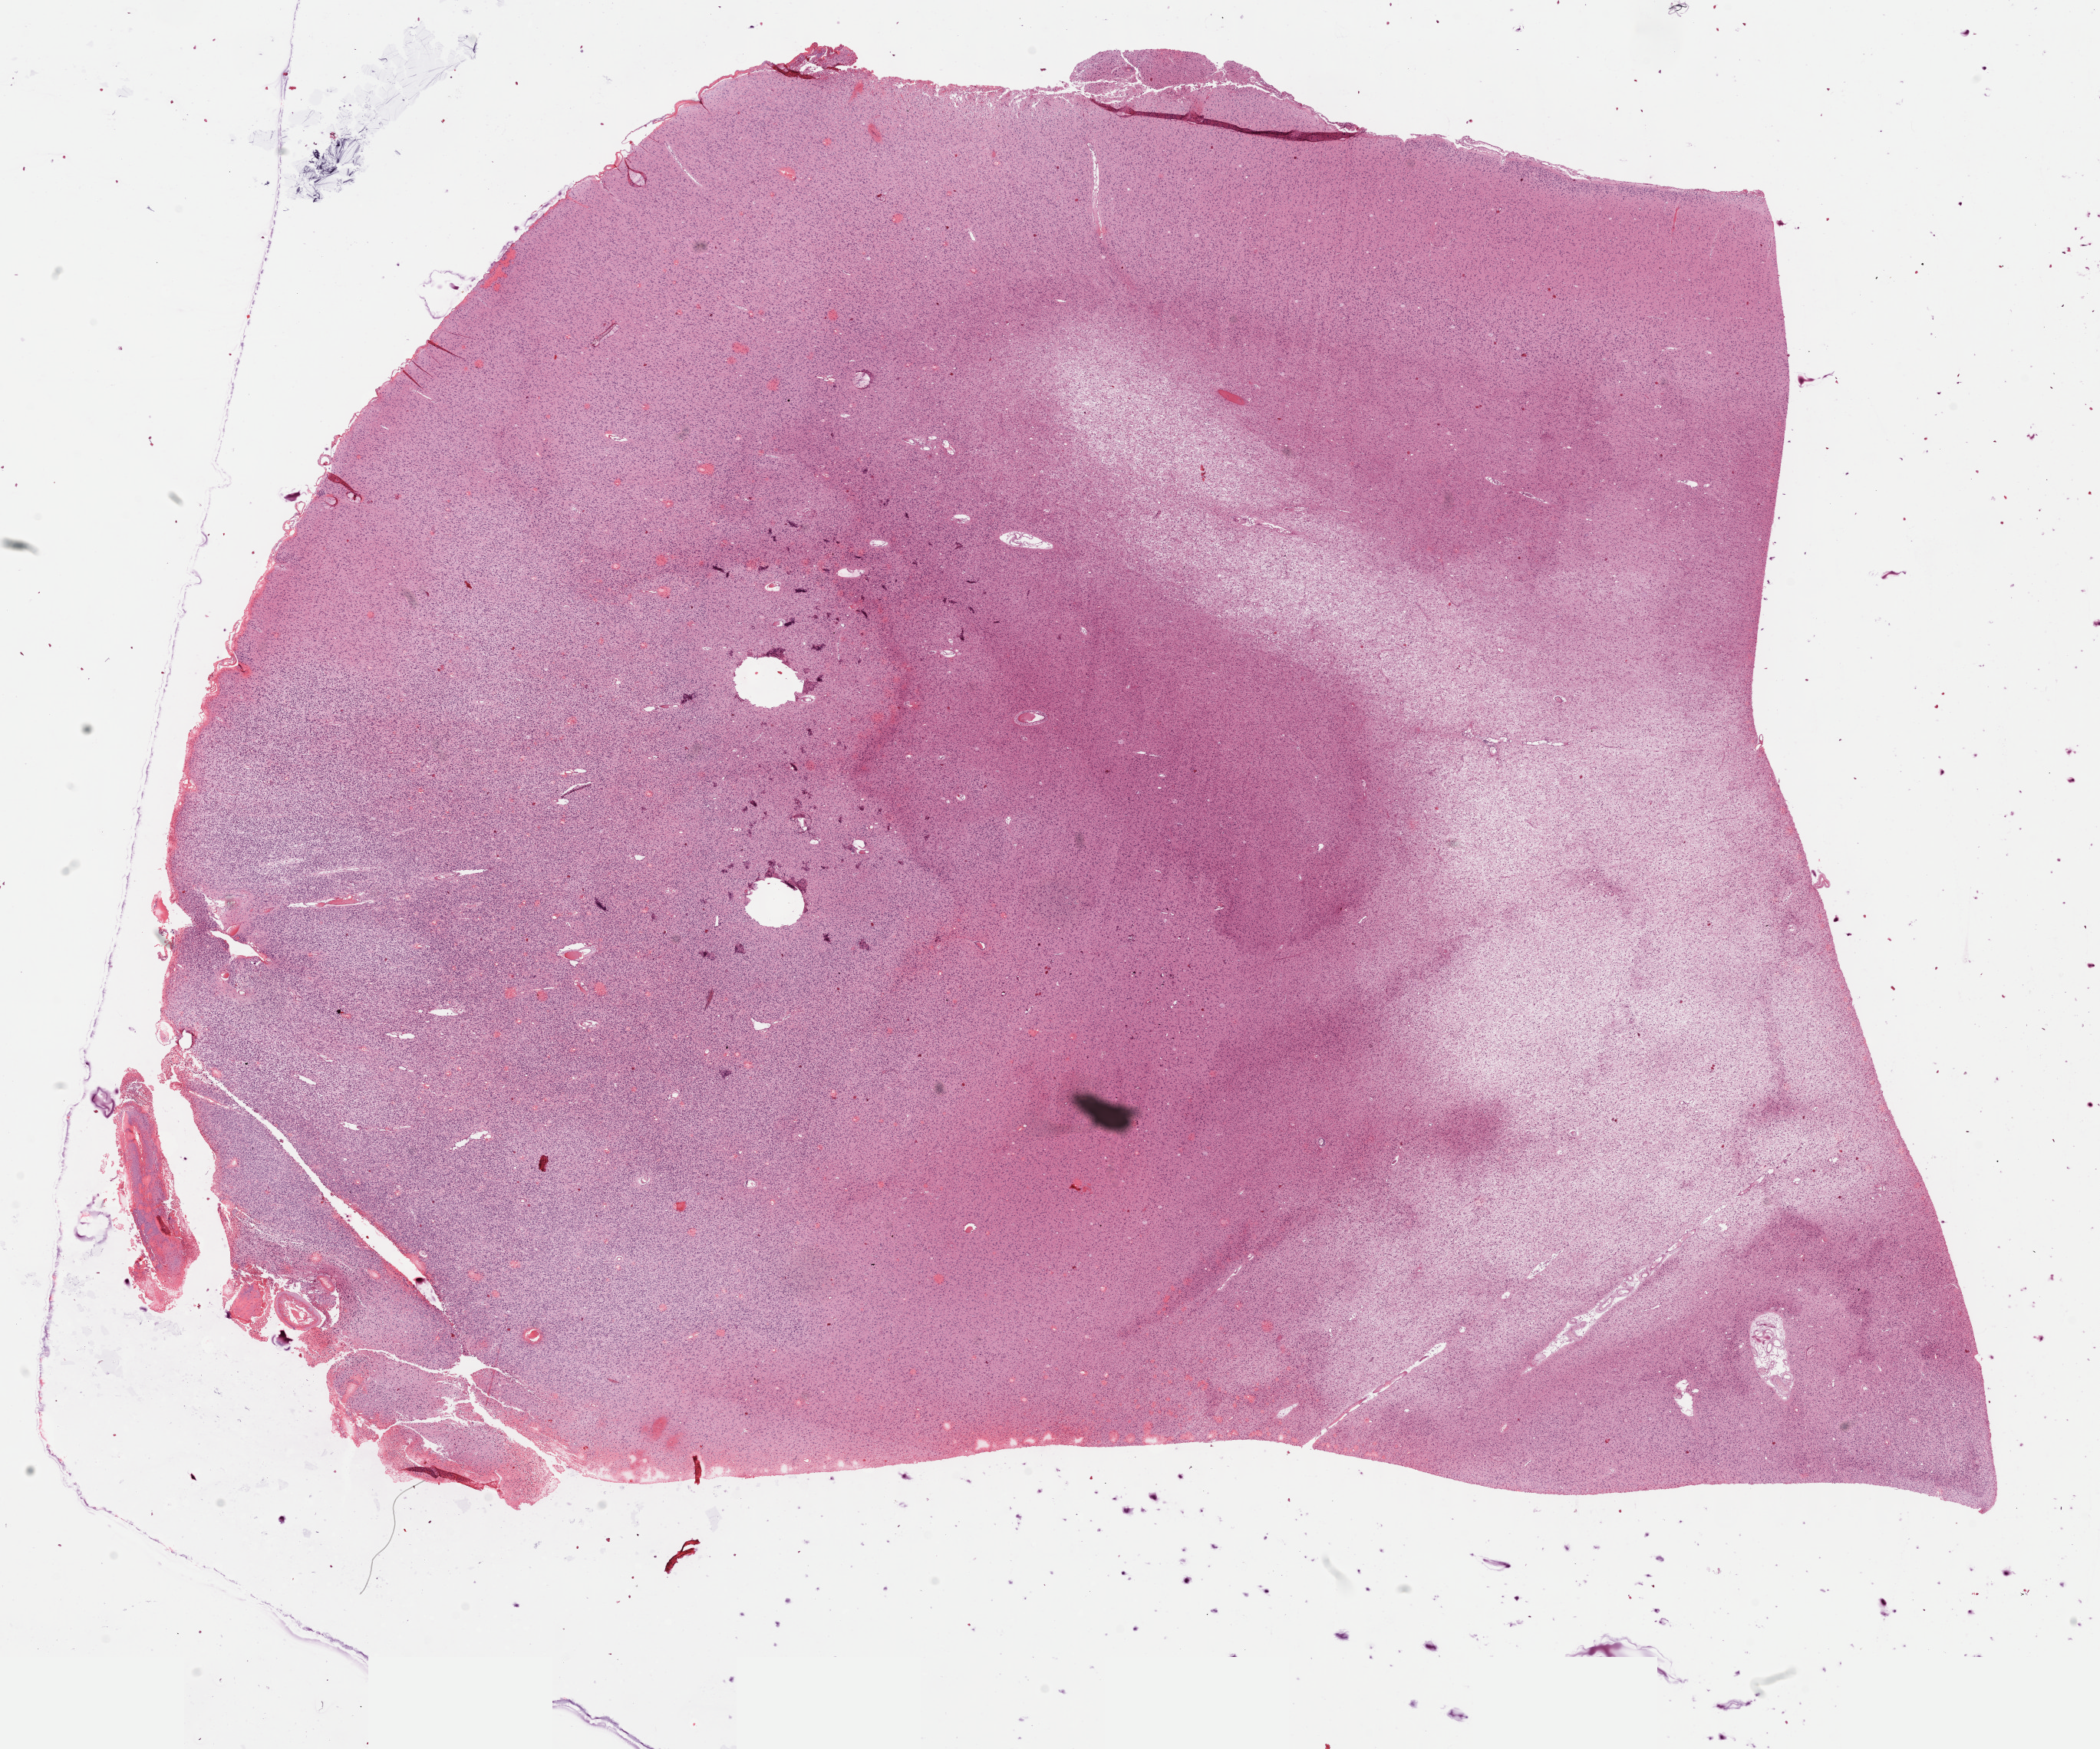
H&E-stained whole-slide image, a low-resolution overview of the entire scanned area, about 21.6 x 18.0 mm (acquisition: 40x scan); FFPE section; primary tumour sample from the brain. Female patient; age at initial diagnosis 52 years.
Histologic diagnosis: Oligodendroglioma, anaplastic (cerebrum).